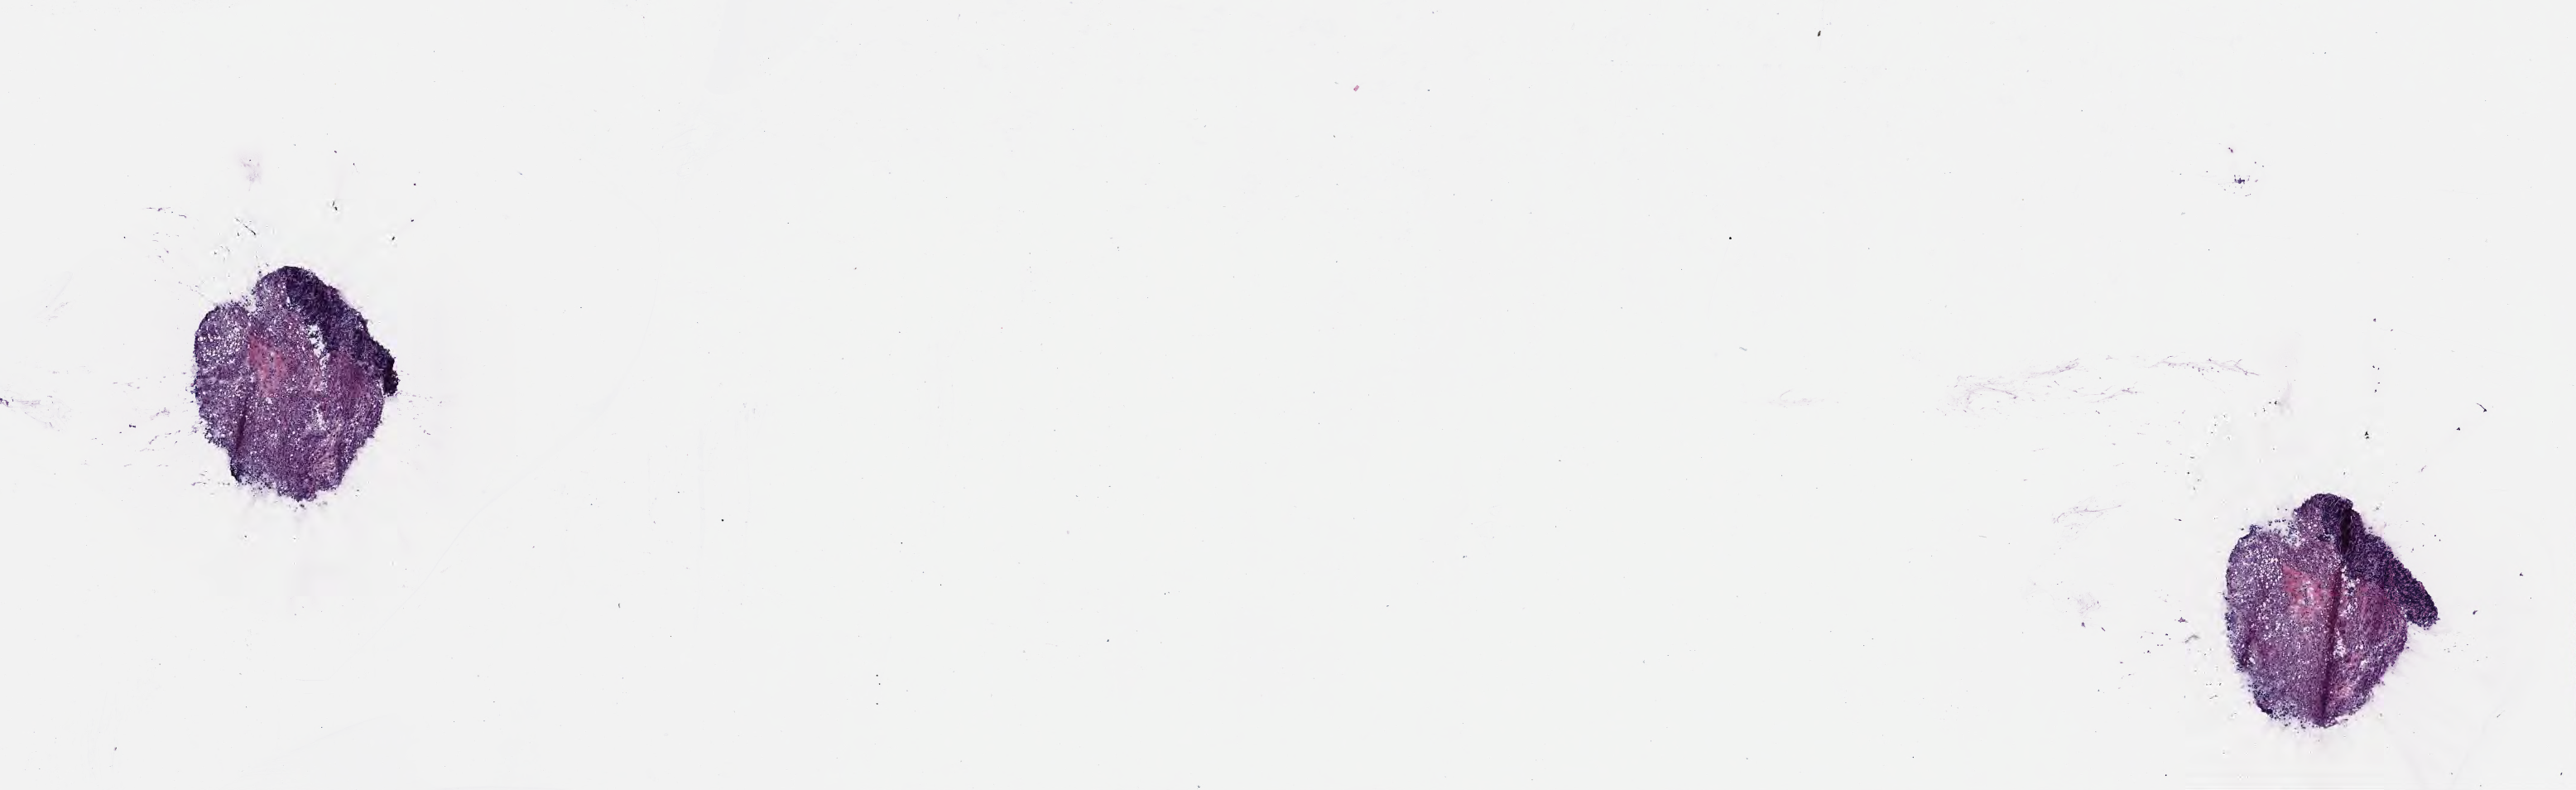
Digitized hematoxylin and eosin (H&E)-stained section, low-resolution overview of the scanned area, about 12.6 x 3.9 mm, frozen section, specimen: primary tumor, anatomic site: liver. Patient: male, age at initial diagnosis 7 years. Composition of this section per pathologist review: tumor cells 40%, tumor nuclei 50%, stromal cells 50%, necrosis 10%, normal cells 0%. Inflammatory infiltration, as recorded: lymphocyte infiltration 50%, monocyte infiltration 20%, neutrophil infiltration 10%.
- Ann Arbor stage (patient): Stage IV
- diagnosis: Burkitt lymphoma, NOS